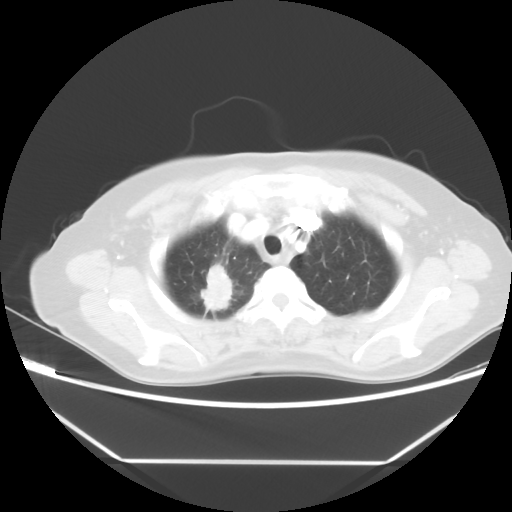
Chest CT, one axial slice; slice 42 of 48 in the series (ordered by position); lung window (W 1500 / L -600 HU); 512 × 512 image matrix, field of view 360 × 360 mm. Female patient, age 65 years. Case-level facts recorded for this patient, not image findings: clinical TNM (as recorded): T1c N1 M1.
Outlined on this slice (bounding box drawn by a radiologist):
- lung tumour (recorded histology: adenocarcinoma): bounding box (x1, y1, x2, y2) in pixels: (200, 261, 232, 312)